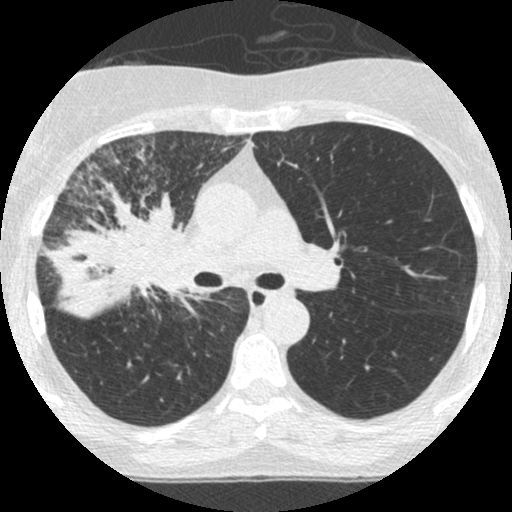
Low-dose screening chest CT, one axial slice. Position 161 of 253 along the scan axis. Lung window (W 1500 / L -600 HU). 512 × 512 image matrix, field of view 294 × 294 mm.
Structures marked on this image (expert manual segmentation):
- lesion 2 (tumor, hilum of right lung): box from (x=41, y=191) to (x=184, y=319) px